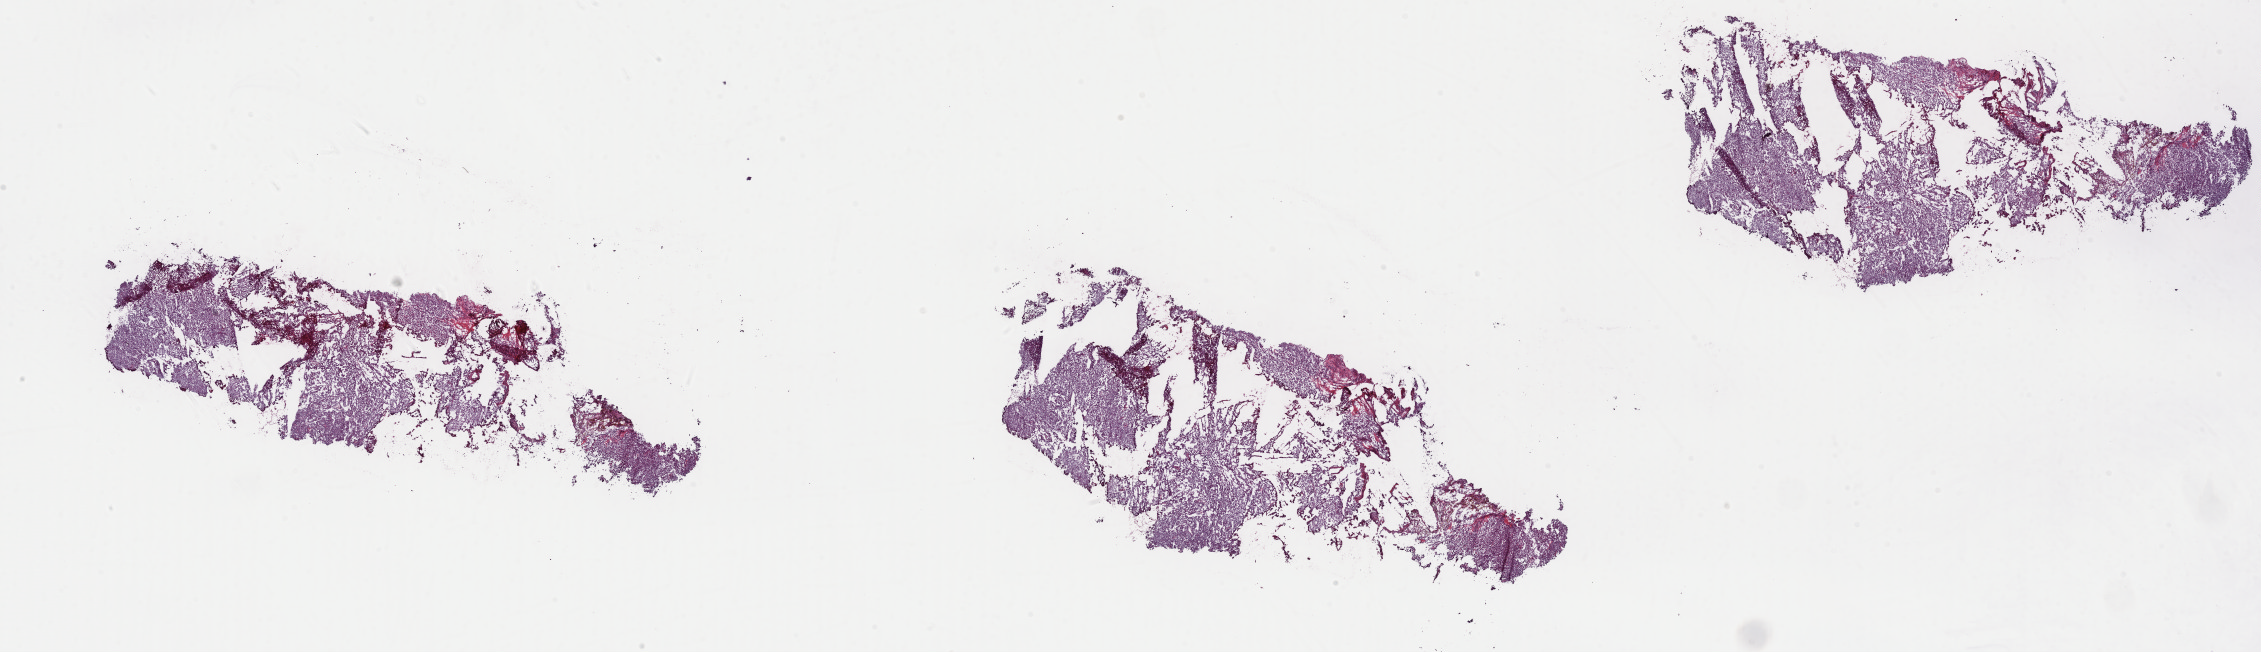
Whole-slide histology image, H&E-stained — shown as a low-resolution overview of the whole scanned area (about 35.7 x 10.3 mm). Frozen section from the top of the tissue portion. Brain, primary tumour sample. Patient: male, age at initial diagnosis 26 years. Histologic grade: G2 (moderately differentiated). Slide review estimates, as recorded: tumour cells 70%, tumour nuclei 80%, normal cells 10%, stromal cells 20%, necrosis 0%. Inflammatory infiltration, as recorded: lymphocyte infiltration 0%, monocyte infiltration 0%, neutrophil infiltration 0%.
Diagnosis: Oligodendroglioma, NOS.